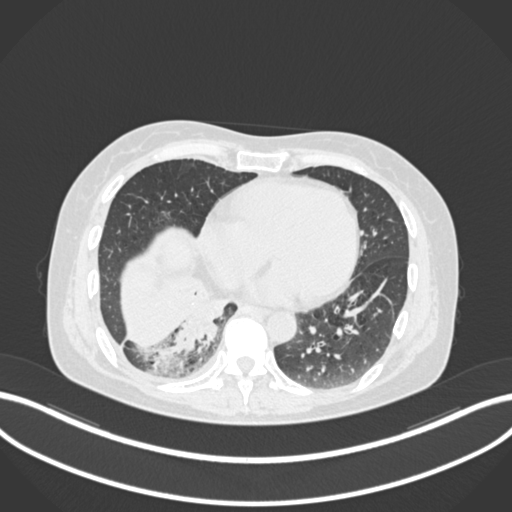
Chest CT, one axial slice. Slice 51 of 168 in the series (ordered by position). Reconstruction kernel B30f. Lung window (W 1500 / L -600 HU). 1 mm slice thickness. 512 × 512 image matrix, field of view 400 × 400 mm. Patient: female, 63 years. From the clinical record (not read from this slice): clinical TNM (as recorded): T1c N0 M0.
Outlined on this slice (bounding box drawn by a radiologist):
- lung tumour (recorded histology: adenocarcinoma): bounding box <173,284,236,355> (left, top, right, bottom; pixels)